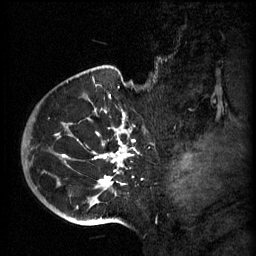
Breast MRI (dynamic contrast-enhanced), one sagittal slice. Position 47 of 60 along the scan axis. 3 images stored at this slice position (order not interpretable as contrast timing). 1.5 T. TE 4.2 ms, TR 11 ms. 2 mm slice thickness. 256 × 256 image matrix, field of view 200 × 200 mm. Female patient, age 51 years.
Annotated regions visible in this slice (semi-automatic segmentation, software-assisted and operator-edited):
- analysis volume of interest (the breast-tissue region the enhancement analysis was run in; not a lesion): box from (x=49, y=82) to (x=153, y=197) px
- tumour enhancement mask (voxels above the 70 % enhancement threshold inside the analysis volume of interest): (x=95, y=108)–(x=133, y=189)